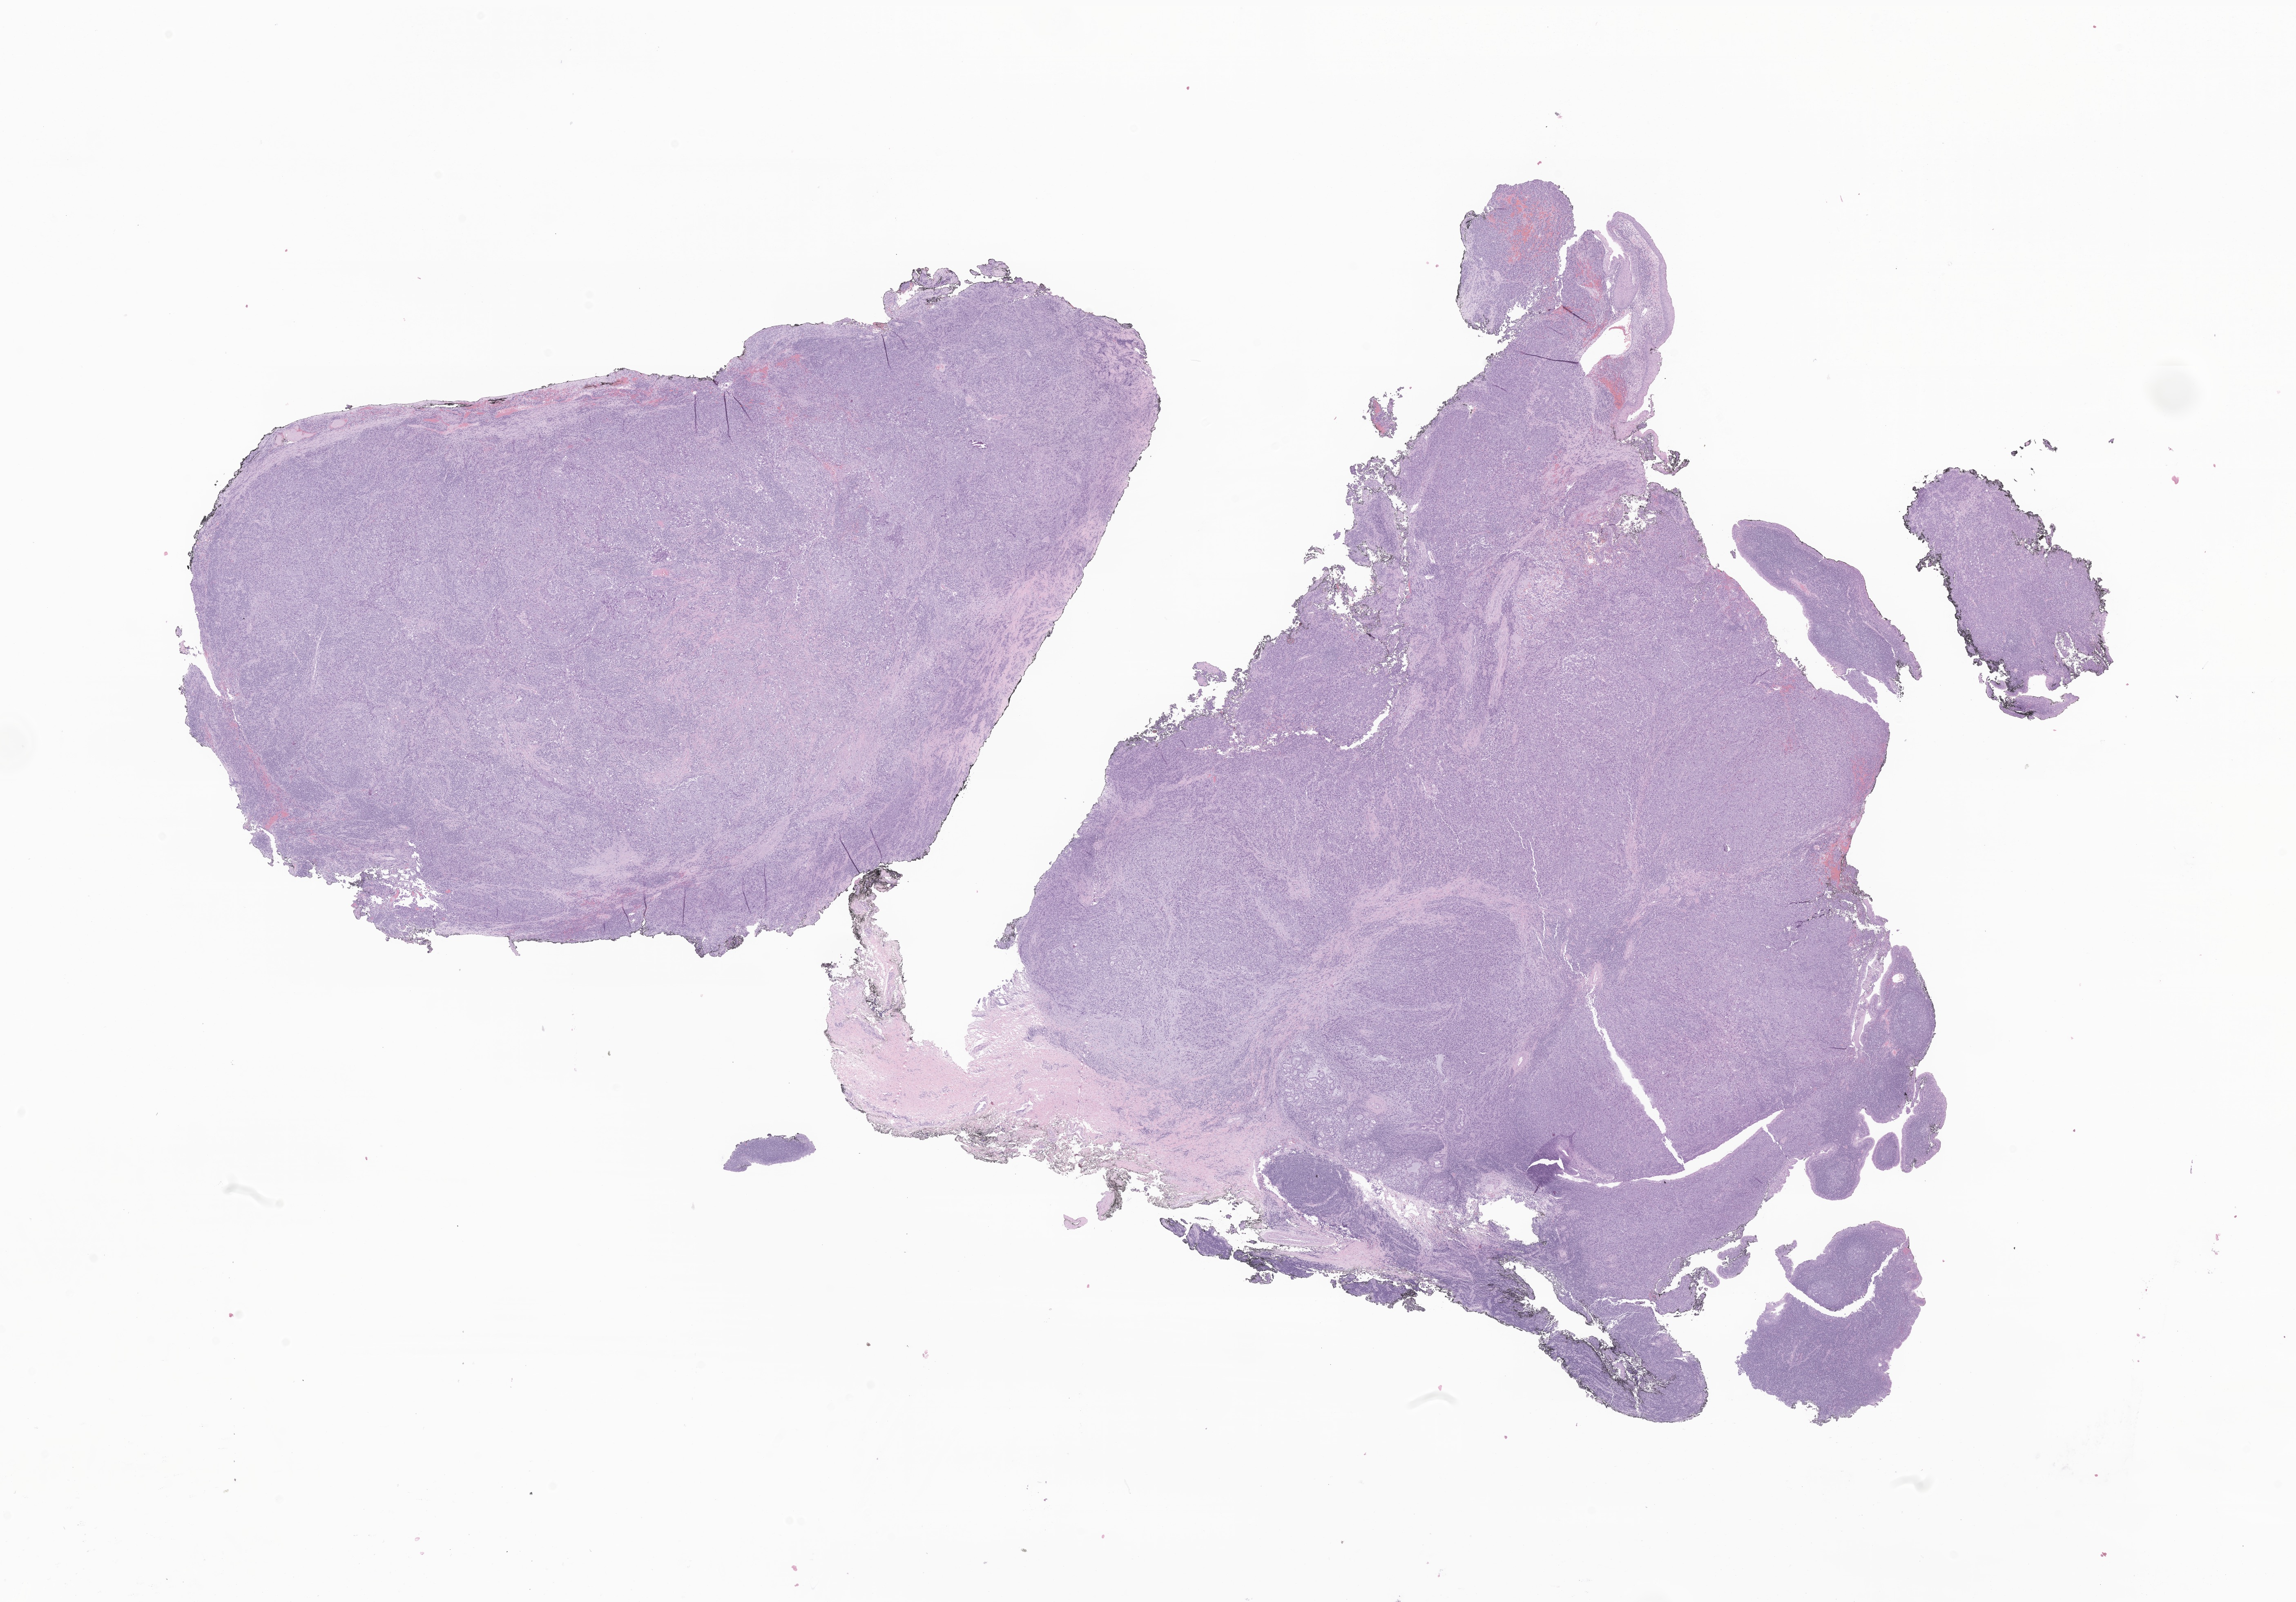
Digitized haematoxylin and eosin-stained section of tumor tissue from the nasopharynx — a low-resolution overview of the entire scanned area, about 23.7 x 16.5 mm; formalin-fixed paraffin-embedded section. Patient male; age 196 months (16 years 4 months).
• diagnosis (ICD-O-3 morphology term): Carcinoma, metastatic, NOS